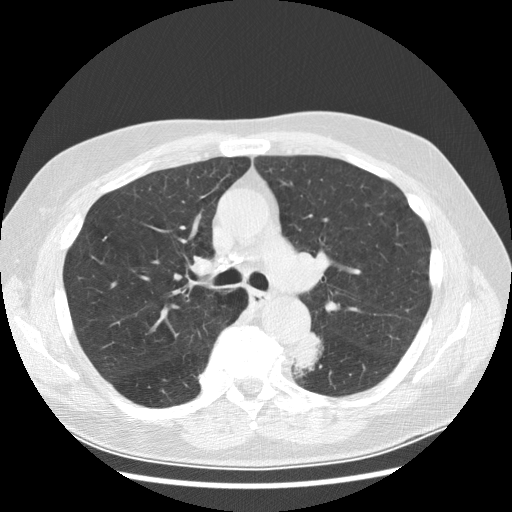
Low-dose screening chest CT, one axial slice; slice 185 of 282 in the series (ordered by position); 120 kVp; lung window (W 1500 / L -600 HU); 2.5 mm slice thickness; 512 × 512 image matrix, field of view 370 × 370 mm.
Structures marked on this image (outlined manually by an expert reader):
- lesion 1 (tumor, lower lobe of left lung): box from (x=293, y=333) to (x=323, y=378) px